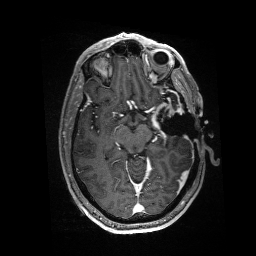
Brain MRI from a brain-tumour surgery series, one axial slice; position 96 of 176 along the scan axis; T1-weighted post-contrast; 1 mm slice thickness; 256 × 256 image matrix, field of view 256 × 256 mm. Case-level facts recorded for this patient, not image findings: histopathology: Glioblastoma; WHO grade: 4; IDH mutation: no.
Annotated regions visible in this slice (outlined manually by an expert reader):
- residual tumour: box from (x=151, y=102) to (x=184, y=130) px